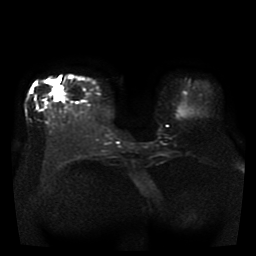
Breast MRI, one axial slice. Position 11 of 41 along the scan axis. Diffusion-weighted series; image 2 of 4 stored at this slice position (different b-values; order by instance number). 1.5 T. 5 mm slice thickness. 256 × 256 image matrix. Female patient.
Structures marked on this image (manually delineated by an expert):
- tumour on diffusion-weighted imaging: box from (x=53, y=86) to (x=63, y=101) px